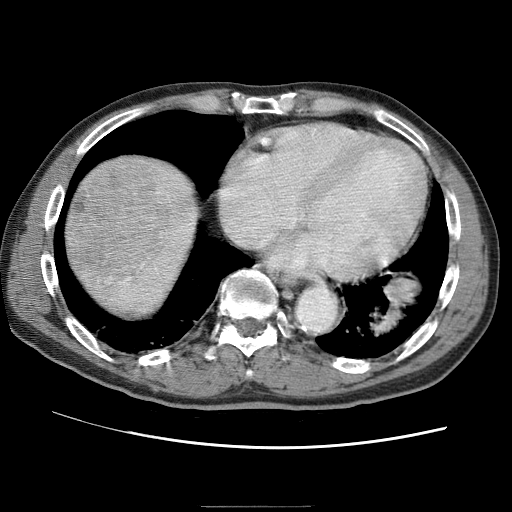
Contrast-enhanced abdominal CT (liver protocol), one axial slice. Position 65 of 75 along the scan axis. Reconstruction kernel STANDARD. 120 kVp. One of 2 acquisitions stored at this slice position. Soft-tissue window (W 400 / L 40 HU). 512 × 512 image matrix, field of view 360 × 360 mm. Case-level facts recorded for this patient, not image findings: diagnosis: hepatocellular carcinoma (patient treated with transarterial chemoembolisation; whether this scan precedes or follows treatment is not stated here); TNM stage (as recorded): Stage-II; Child-Pugh class: A; tumour nodularity: multinodular; tumour size: 2 cm.
Annotated regions visible in this slice (semi-automatically segmented with operator editing):
- liver parenchyma outside the tumour (the mass and vessels are separate outlines, so this box may not span the whole liver): bounding box <62,150,206,320> (left, top, right, bottom; pixels)
- mass: <64,156,173,292>
- liver vessels: <95,154,144,168>